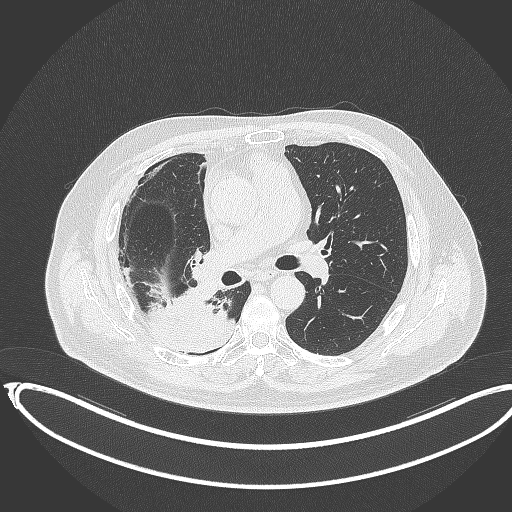
Chest CT, one axial slice; position 201 of 403 along the scan axis; 120 kVp; lung window (W 1500 / L -600 HU); 512 × 512 image matrix, field of view 436 × 436 mm. Male patient, age 68 years. From the clinical record (not read from this slice): clinical TNM (as recorded): T2a N0 M0.
Outlined on this slice (bounding box drawn by a radiologist):
- lung tumour (recorded histology: adenocarcinoma): box from (x=150, y=287) to (x=235, y=357) px